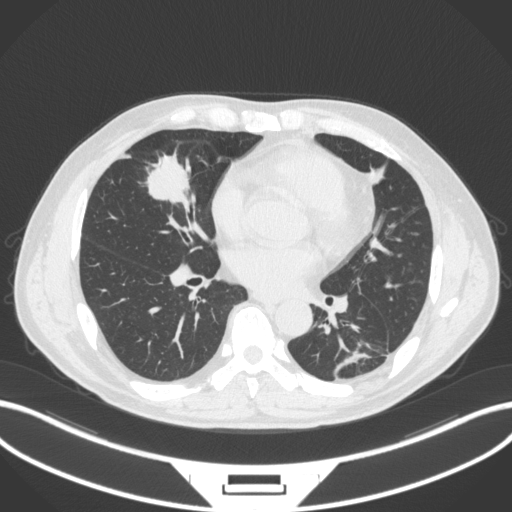
Chest CT, one axial slice; position 133 of 399 along the scan axis; 120 kVp; lung window (W 1500 / L -600 HU); 1 mm slice thickness; 512 × 512 image matrix. Patient: male, 59 years. Case-level facts recorded for this patient, not image findings: clinical TNM (as recorded): T2a N1 M0.
Outlined on this slice (rectangle marked by the reading radiologist):
- lung tumour (recorded histology: adenocarcinoma): bounding box <136,145,200,211> (left, top, right, bottom; pixels)